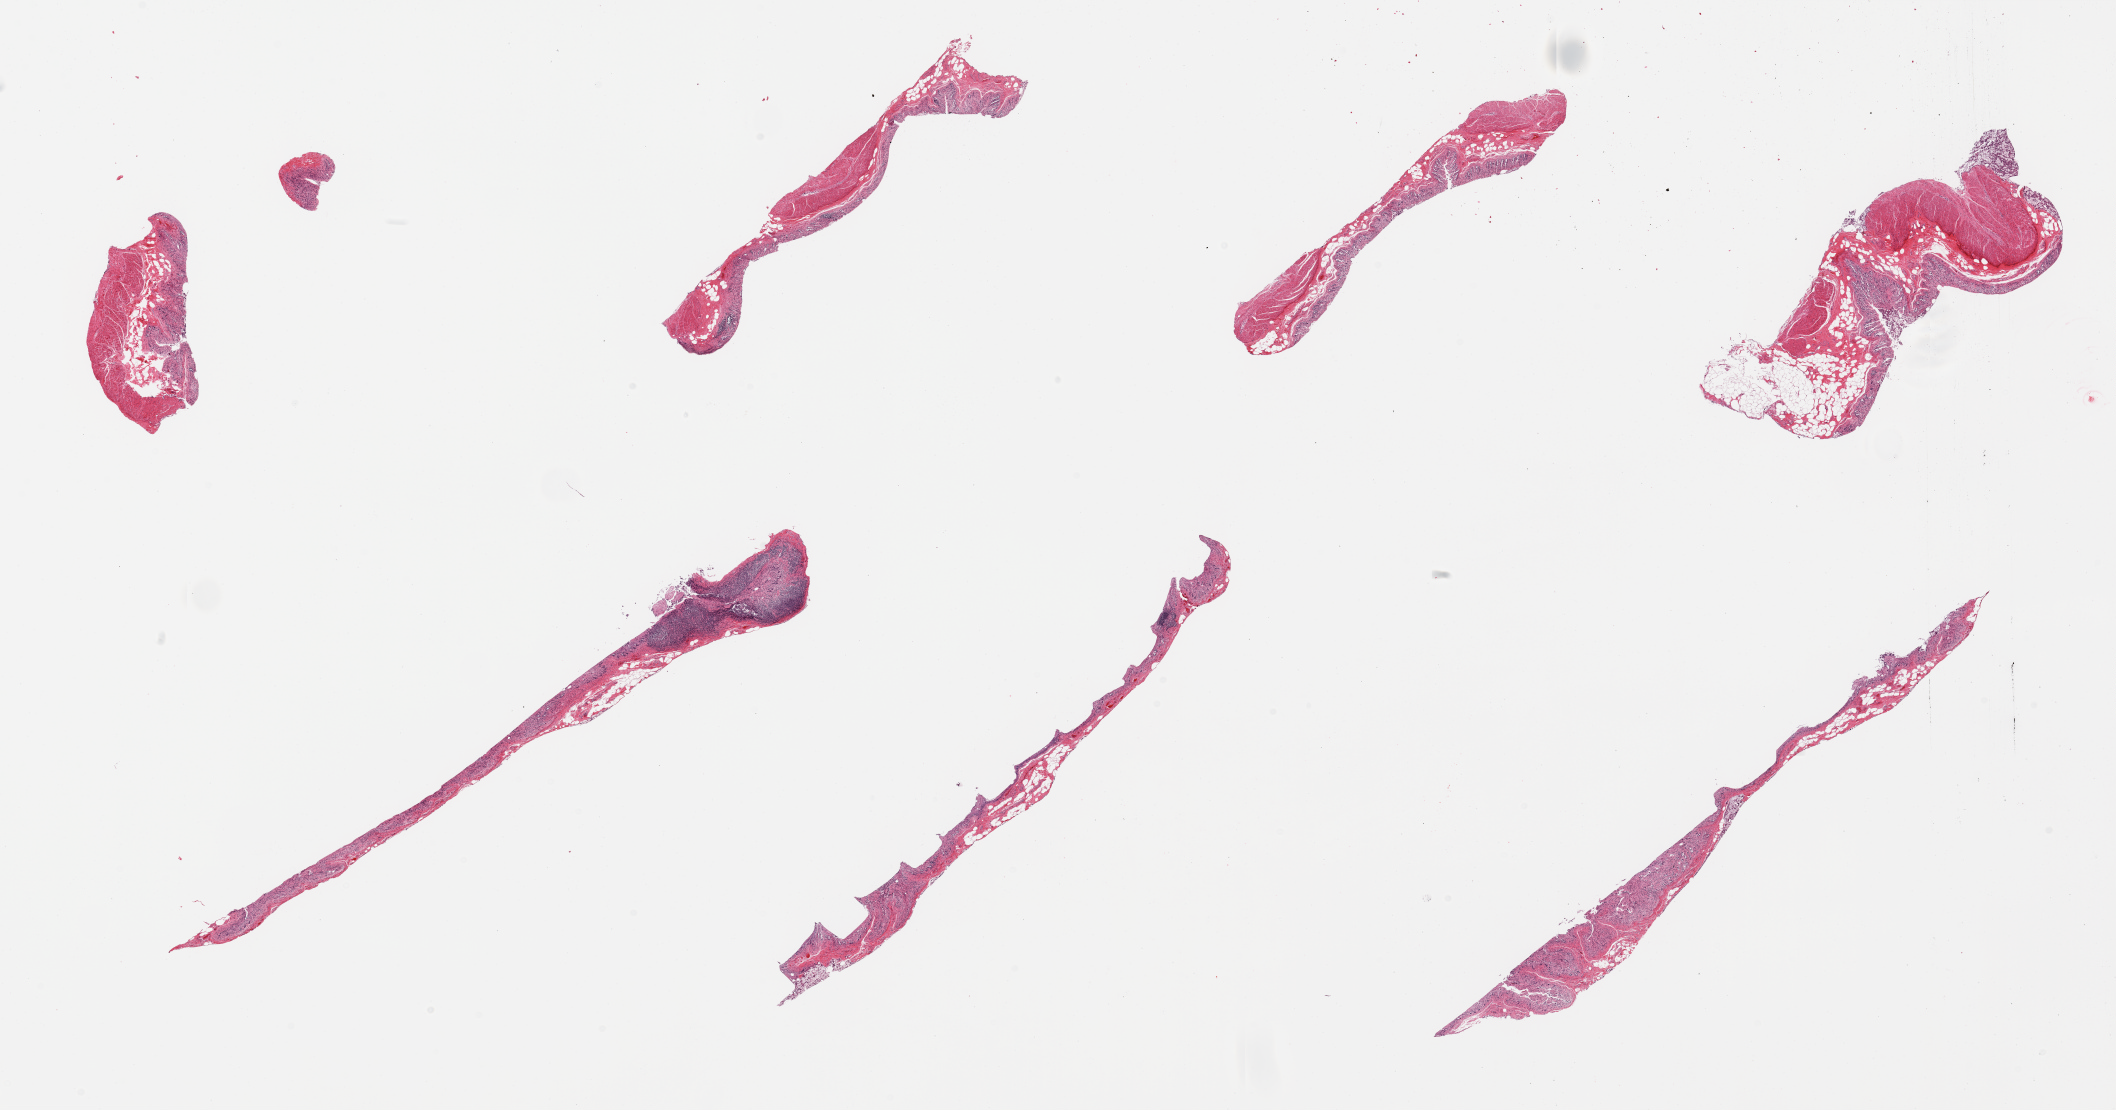
Digitized haematoxylin and eosin-stained section, brightfield, whole scanned area (about 33.5 x 17.6 mm, acquisition: 20x scan) shown as a low-resolution overview, PAXgene-fixed paraffin-embedded (PFPE) section, sampled site (target tissue): transverse colon, tissue donor sample. Donor sex: male.
Reviewer comment on this tissue sample: 7 pieces; mucosa = 3, muscularis = 2; muscle missing on 3 of 7.